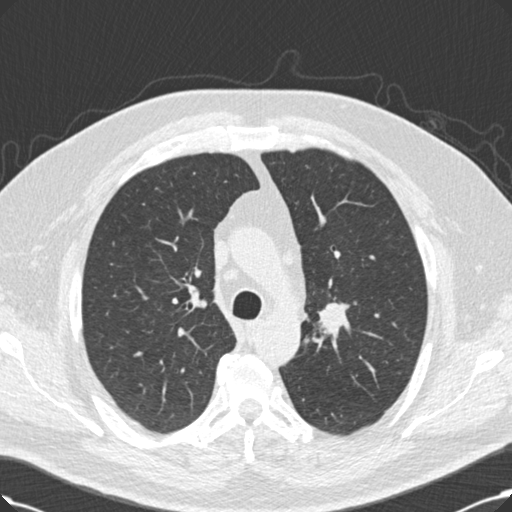
Chest CT (low-dose screening protocol), one axial image. Third screening round (two years after baseline). Lung window (W 1500 / L -600 HU). 2 mm slice thickness. 512 × 512 image matrix, field of view 365 × 365 mm. Male, age 60 years at enrolment. Current smoker at enrolment.
Expert reader's lesion annotation, bounding box (x1, y1, x2, y2) in pixels: (318, 297, 349, 331). The exam's reader record, not a measurement of the box and not confirmed to be the same lesion: non-calcified nodule or mass ≥4 mm, left upper lobe, 20 × 20 mm, smooth margins, soft tissue attenuation, pre-existing on the prior screen: no. Lung cancer was diagnosed 53 days after this screen: squamous cell carcinoma, NOS, right upper lobe, 27 mm at pathology.